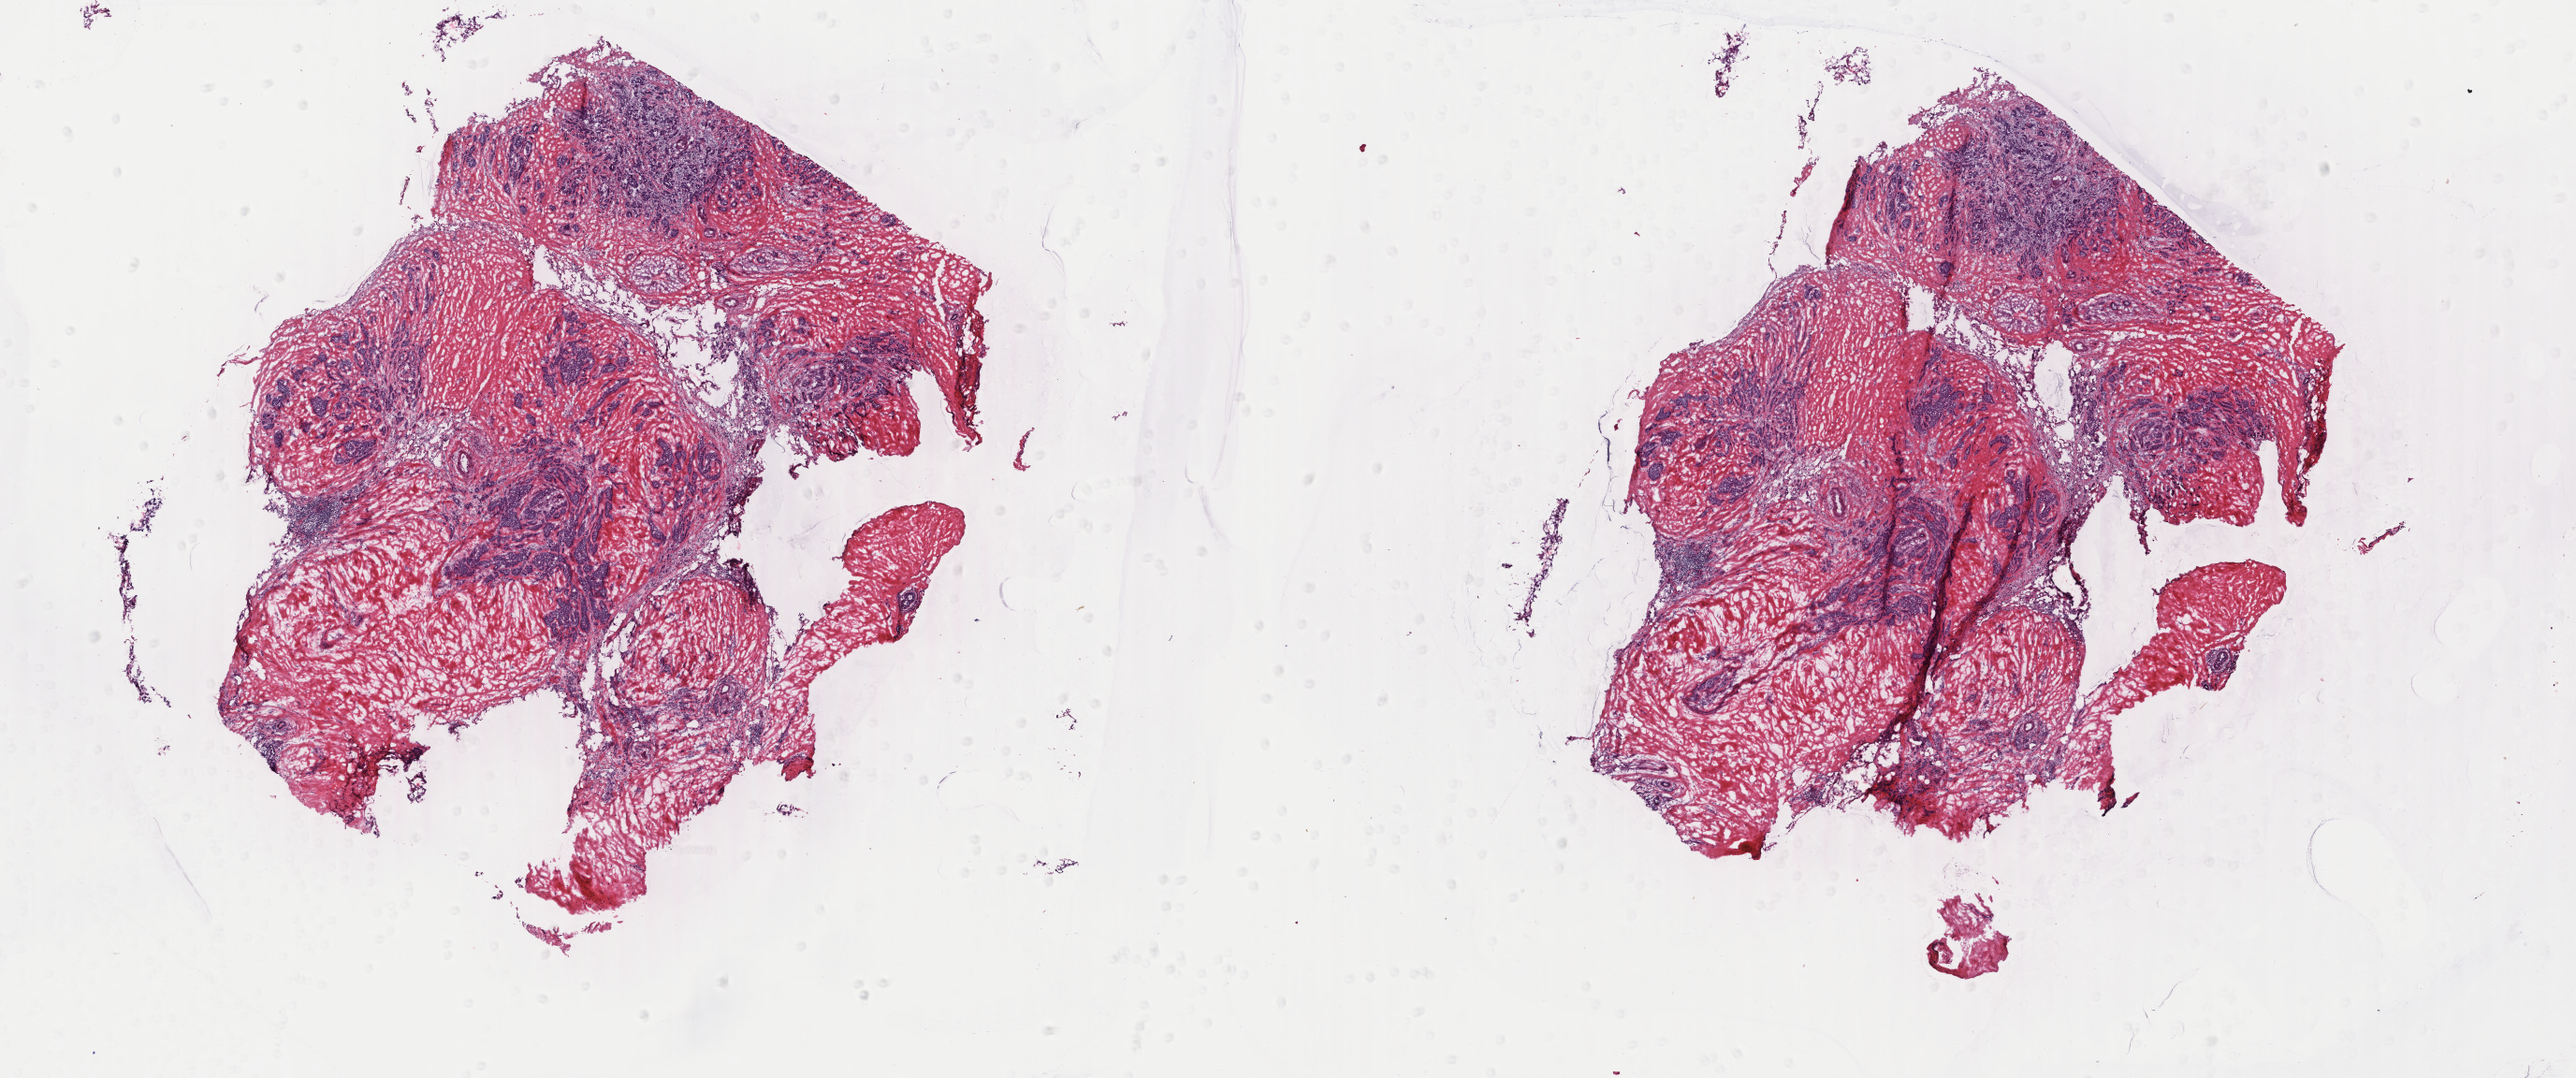
Whole-slide histology image, H&E-stained — shown as a low-resolution overview of the whole scanned area (about 21.9 x 9.2 mm). Frozen section. Sample: primary tumour, breast. Female patient; age at initial diagnosis 80 years. Pathologist review of this section (percent, as recorded): tumour cells 55%, tumour nuclei 65%, normal cells 5%, stromal cells 40%, necrosis 0%. Inflammatory infiltration, as recorded: lymphocyte infiltration 2%, monocyte infiltration 0%, neutrophil infiltration 0%.
- histologic diagnosis: Infiltrating duct carcinoma, NOS
- lymph nodes positive (case pathology): 0 of 6 examined
- AJCC pathologic stage: IA (6th edition)